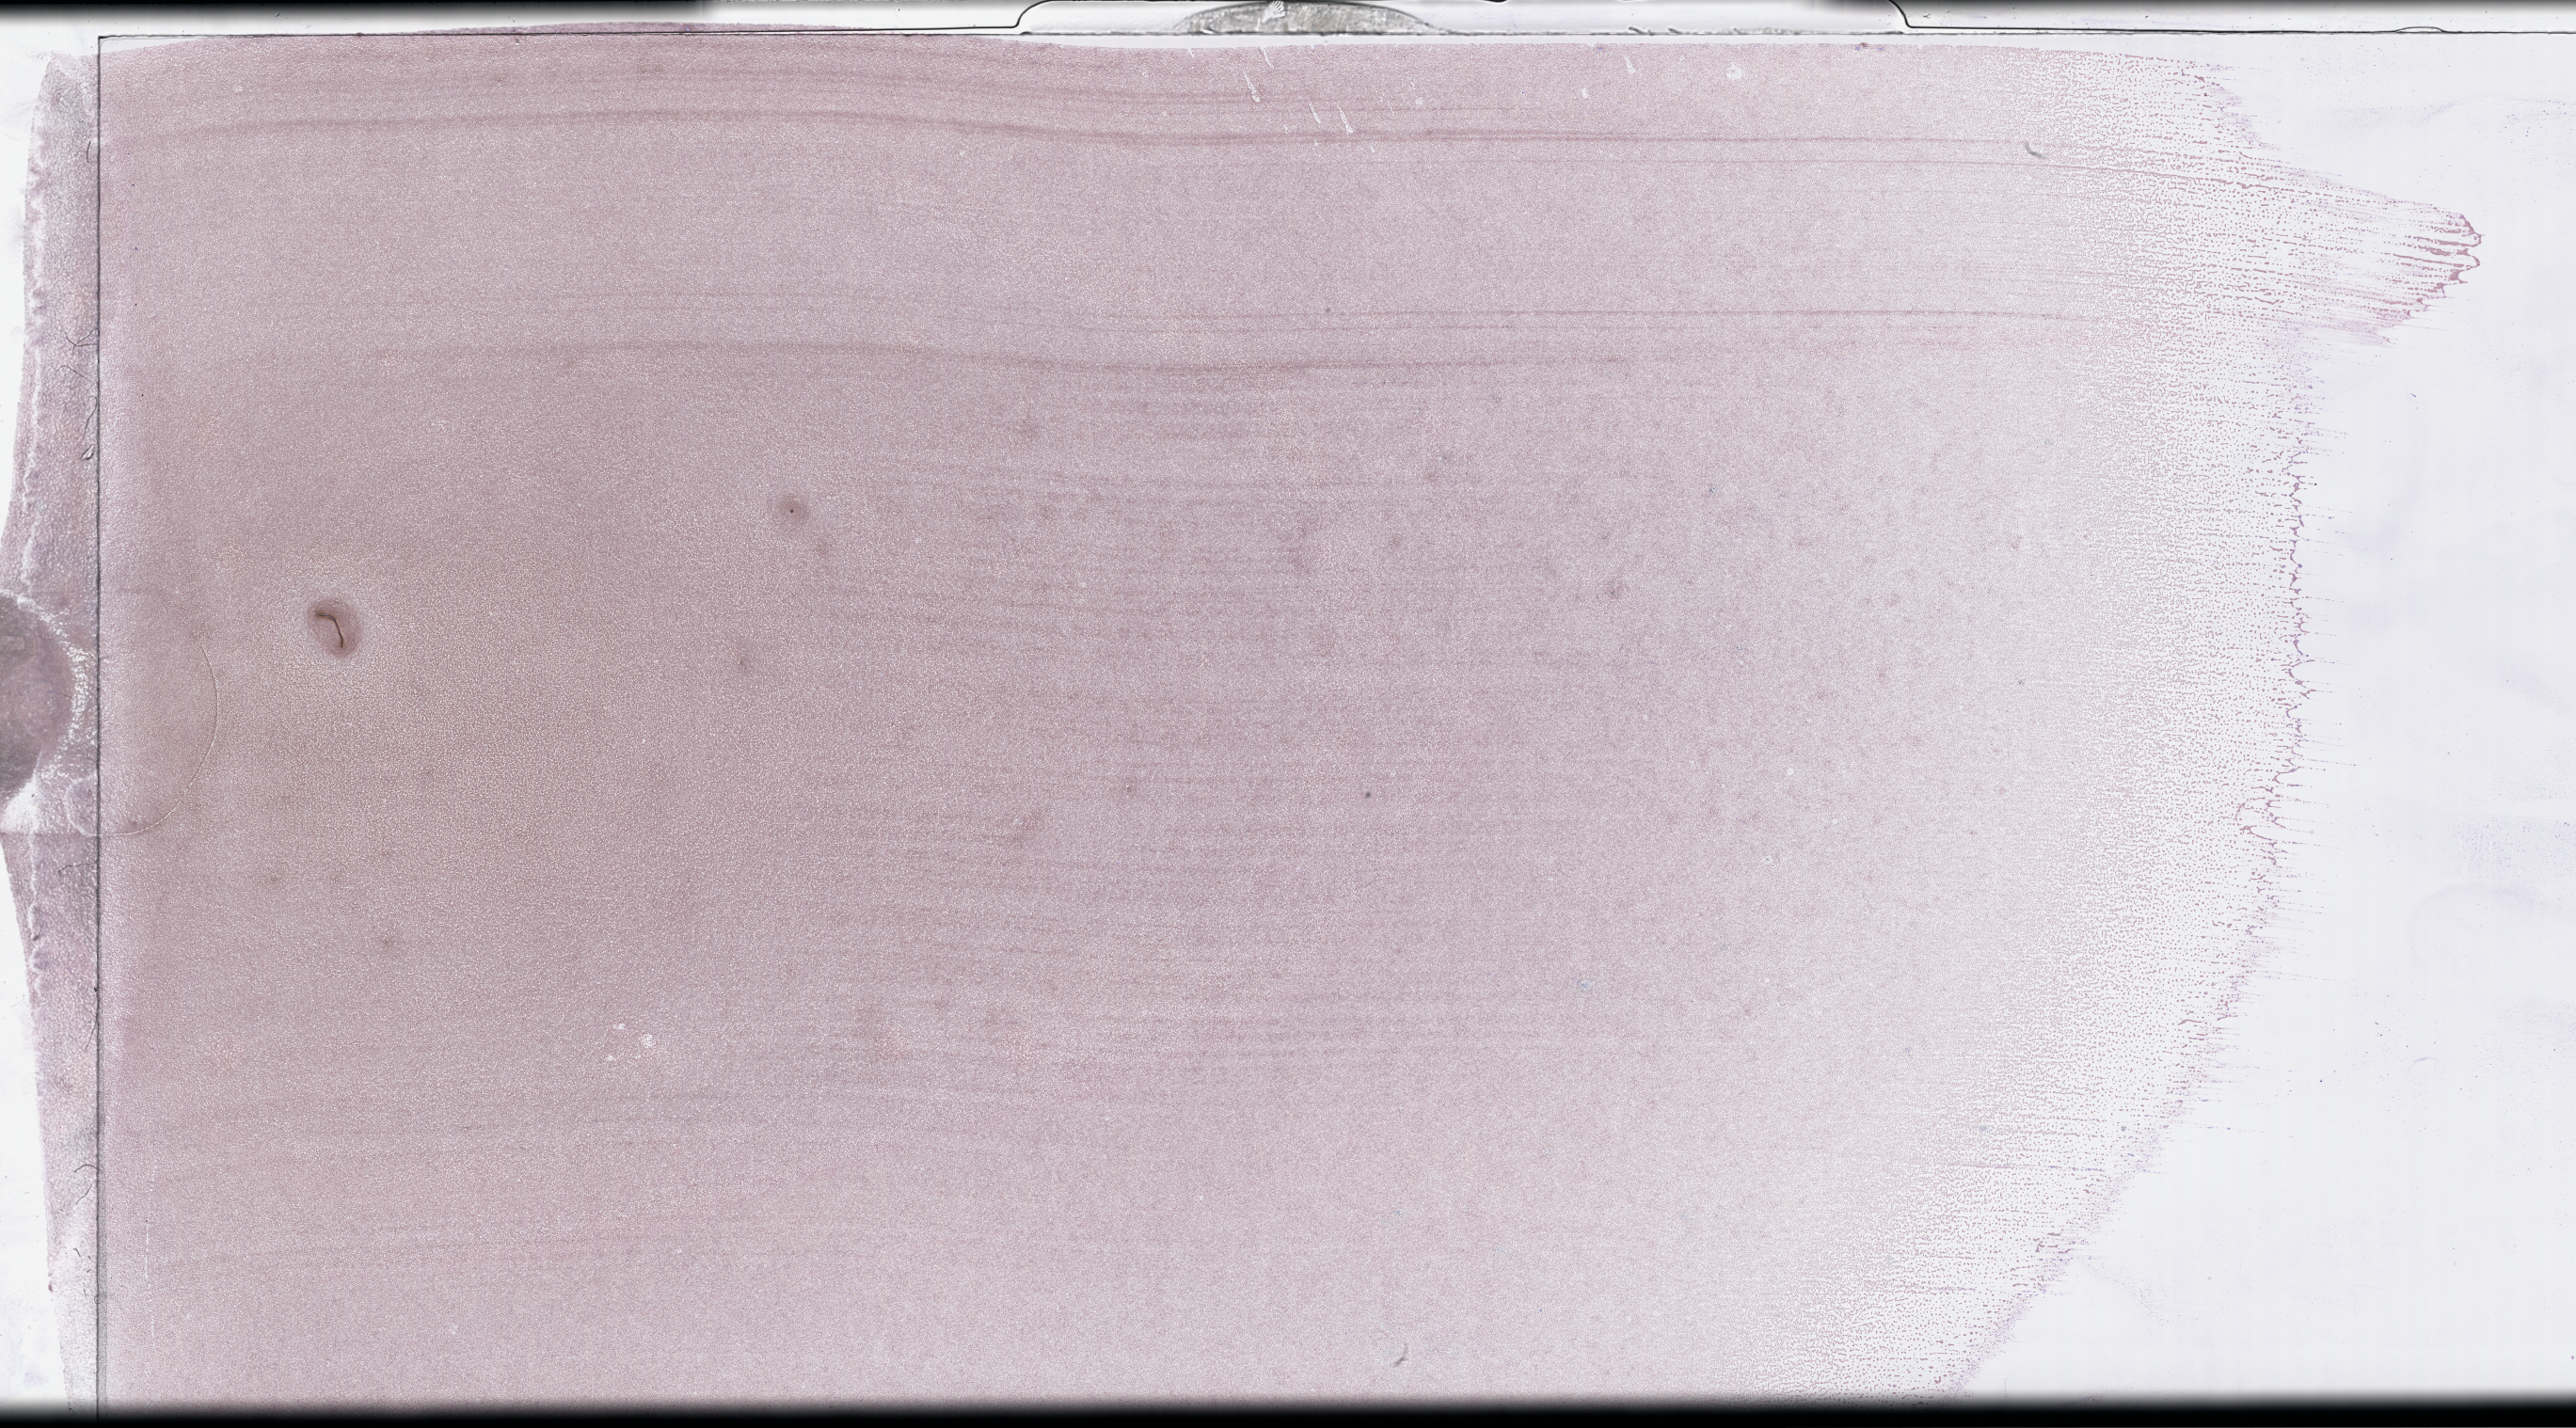
Wright–Giemsa-stained whole blood smear, whole-slide image, low-resolution overview of the scanned area, about 44.2 x 24.5 mm, smear from an EDTA sample, specimen time point: collected at baseline (before treatment). Patient sex: male.
From a patient with: Plasma Cell Myeloma.